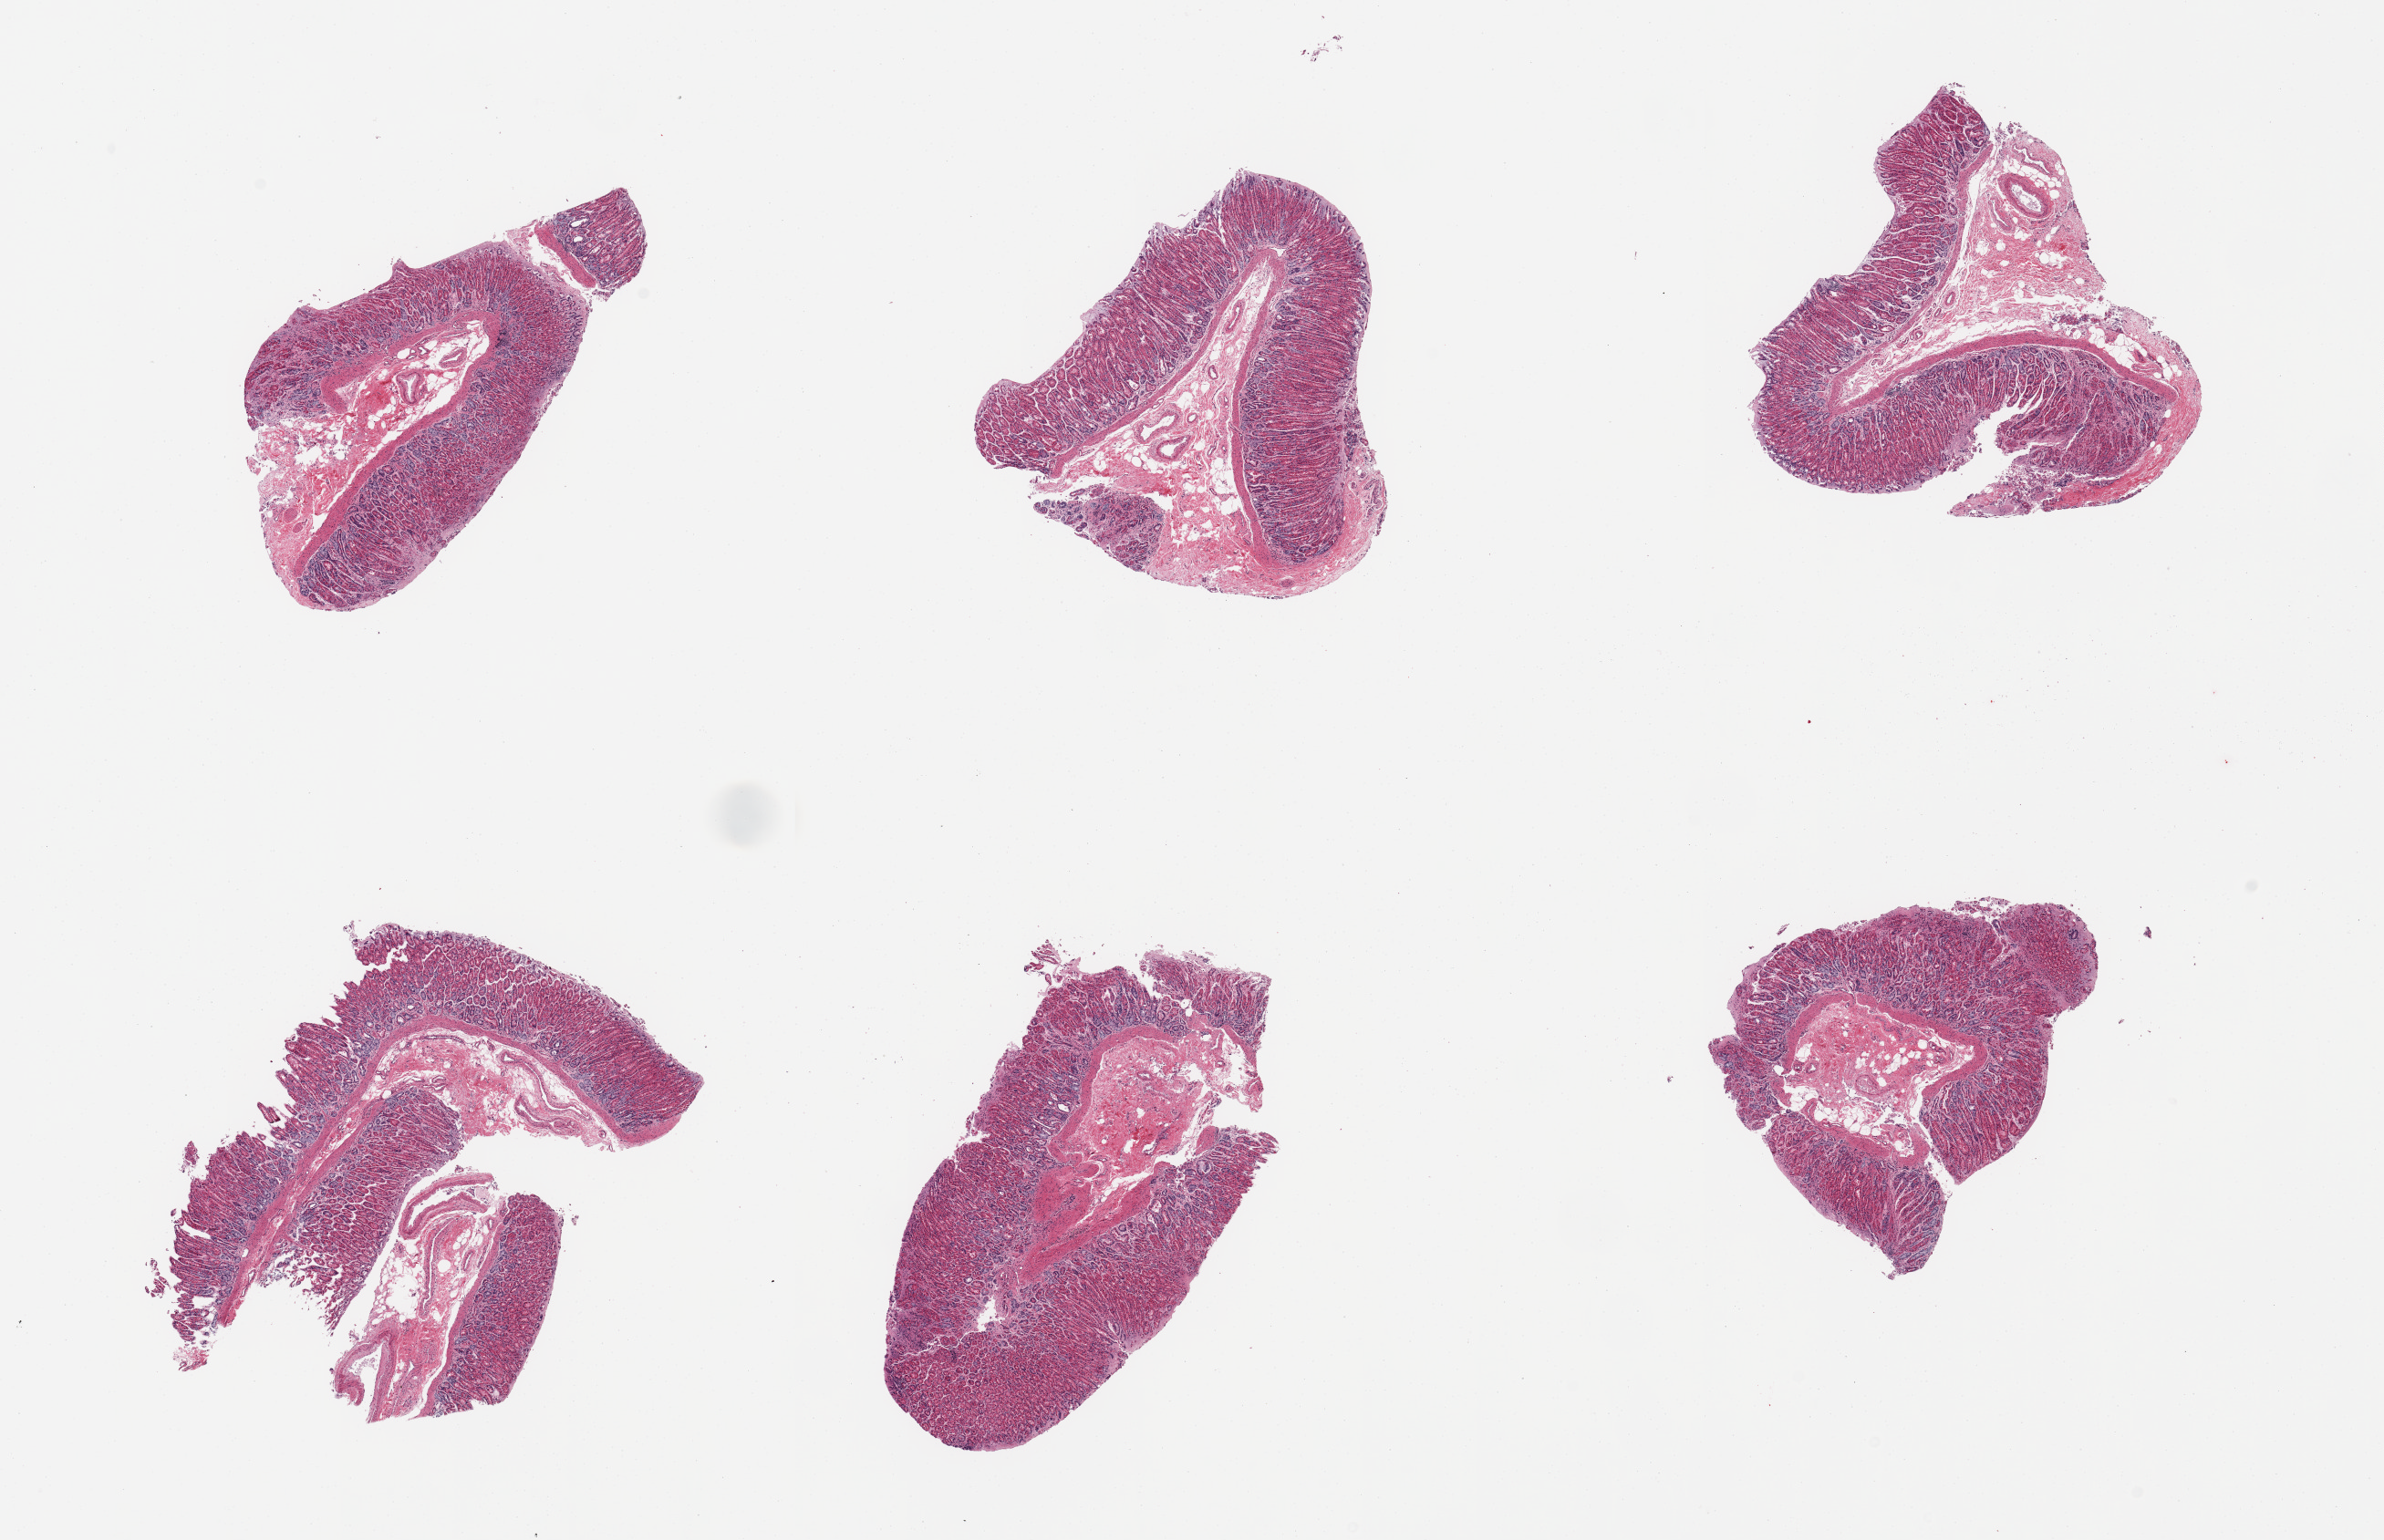
H&E whole-slide image — a low-resolution overview of the entire scanned area, about 20.7 x 13.4 mm (slide scanned at 20x); PAXgene-fixed paraffin-embedded (PFPE) section; section of stomach (target tissue); tissue donor sample.
Reviewer comment on this tissue sample: 6 pieces; superficial foveolar cells sloughed.